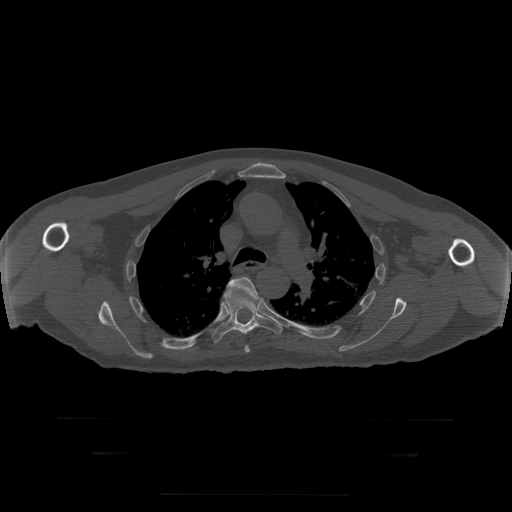
CT including the spine, one axial slice; slice 213 of 397 in the series (ordered by position); 120 kVp; bone window (W 1800 / L 400 HU); 1.25 mm slice thickness; 512 × 512 image matrix, field of view 510 × 510 mm. Patient age 73 years. From the clinical record (not read from this slice): primary cancer: prostate.
Outlined on this slice (semi-automatically segmented with operator editing):
- T5 vertebra: bounding box (x1, y1, x2, y2) in pixels: (229, 277, 260, 353)
- T6 vertebra: (212, 292, 283, 344)